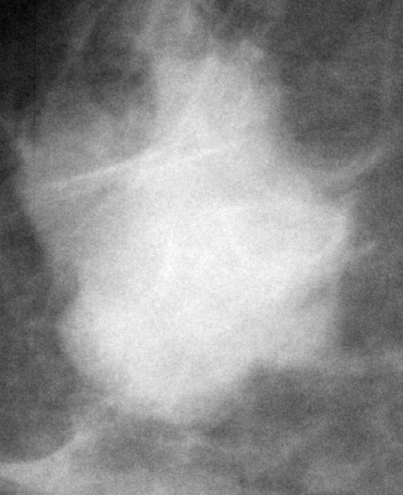
Region of interest cut from a scanned film mammogram (one marked finding), right breast, MLO view, BI-RADS breast density category 3 (scale 1–4).
- Finding: mass, shape irregular, margins microlobulated; BI-RADS assessment category 5; pathology result (as recorded, not read from the image): malignant.